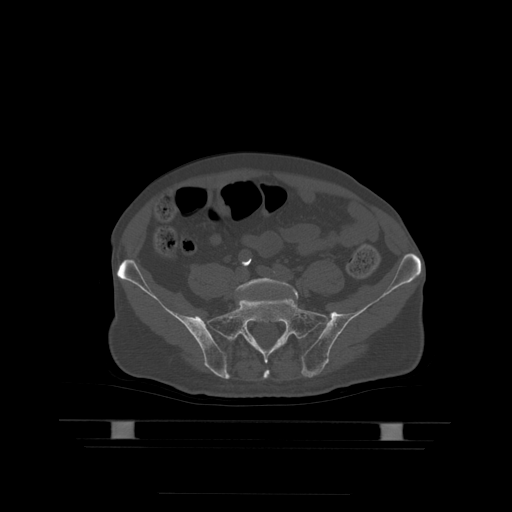
CT including the spine, one axial slice; position 56 of 522 along the scan axis; bone window (W 1800 / L 400 HU); 1.25 mm slice thickness; 512 × 512 image matrix, field of view 436 × 436 mm. Patient age 68 years. From the clinical record (not read from this slice): primary cancer: urothelial.
Structures marked on this image (semi-automatically segmented with operator editing):
- L5 vertebra: bounding box (x1, y1, x2, y2) in pixels: (236, 278, 298, 298)